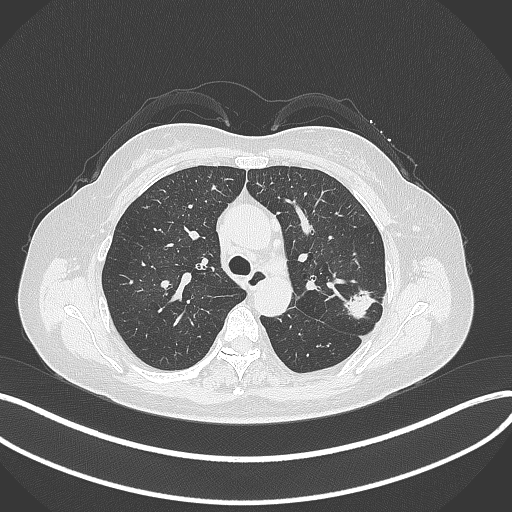
Chest CT, one axial slice; position 224 of 319 along the scan axis; reconstruction kernel B70f; lung window (W 1500 / L -600 HU); 1 mm slice thickness; 512 × 512 image matrix, field of view 400 × 400 mm. Patient: female, 60 years. Case-level facts recorded for this patient, not image findings: clinical TNM (as recorded): T1c N0 M0.
Structures marked on this image (bounding box drawn by a radiologist):
- lung tumour (recorded histology: adenocarcinoma): bounding box (x1, y1, x2, y2) in pixels: (340, 284, 377, 323)